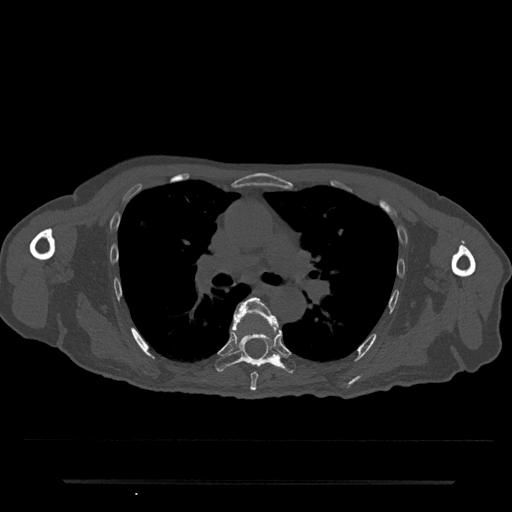
CT including the spine, one axial slice; position 500 of 797 along the scan axis; reconstruction kernel Br40s/3; bone window (W 1800 / L 400 HU); 0.5 mm slice thickness; 512 × 512 image matrix, field of view 427 × 427 mm. Patient: male, 74 years. Case-level facts recorded for this patient, not image findings: primary cancer: prostate.
Structures marked on this image (semi-automatic segmentation, software-assisted and operator-edited):
- T6 vertebra: bounding box (x1, y1, x2, y2) in pixels: (232, 297, 279, 391)
- T7 vertebra: (215, 328, 296, 373)